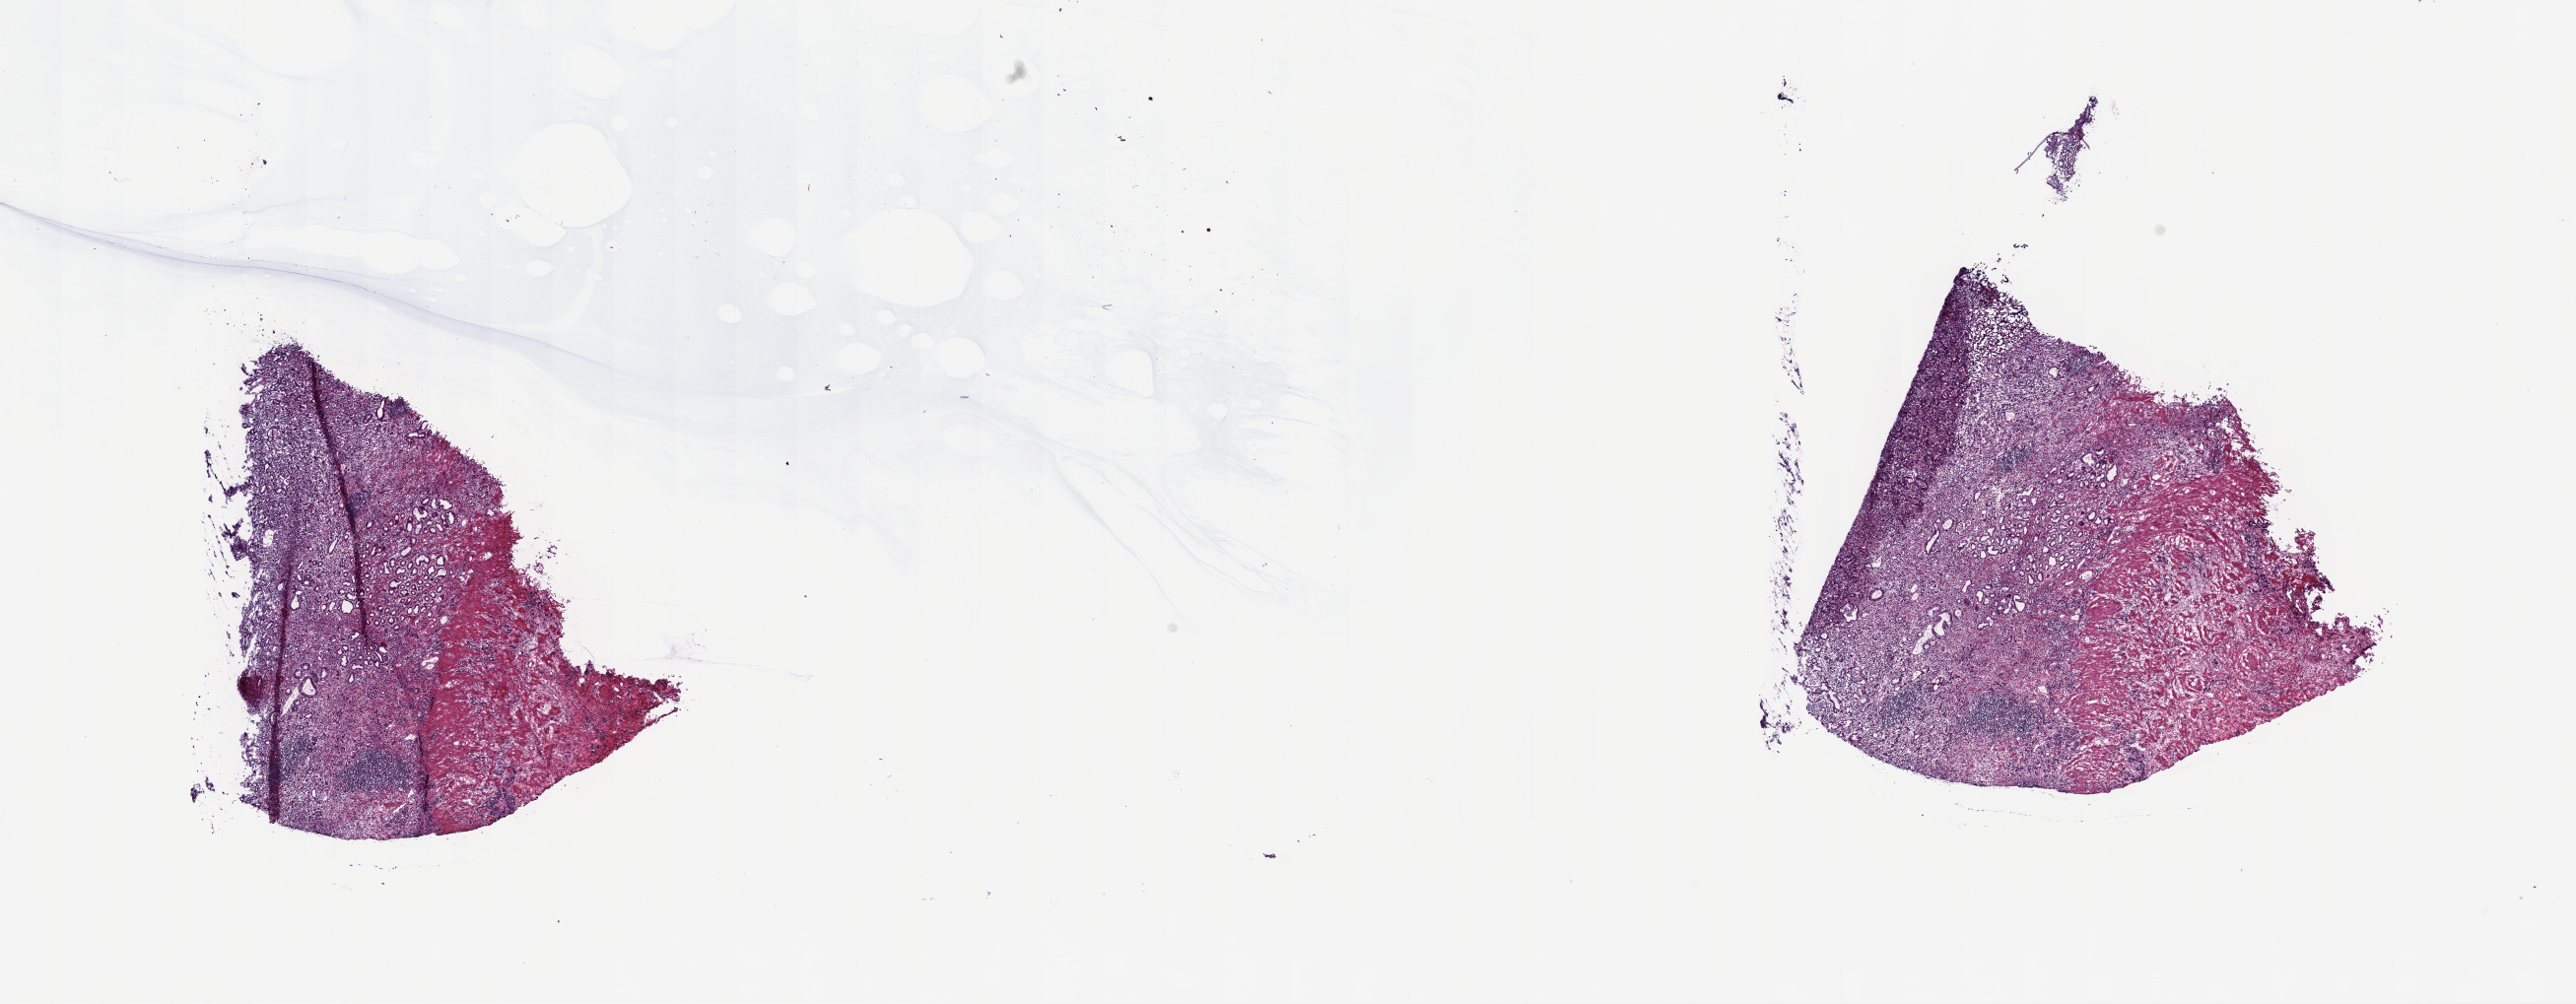
Whole-slide histology image, H&E-stained — low-resolution overview of the scanned area, about 21.1 x 8.2 mm (acquisition: 40x scan). Frozen section from the top of the tissue portion. Primary tumour sample from the stomach. Female, age 72 years at initial diagnosis. Histologic grade: G2 (moderately differentiated). Composition of this section per pathologist review: tumour cells 50%, tumour nuclei 60%, normal cells 30%, stromal cells 20%, necrosis 0%. Inflammatory infiltration, as recorded: lymphocyte infiltration 0%, monocyte infiltration 0%, neutrophil infiltration 0%.
- AJCC pathologic stage: IIB
- lymph nodes positive (case pathology): 0 of 19 examined
- pathologic diagnosis: Adenocarcinoma, intestinal type